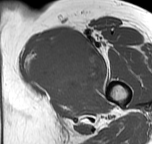
MRI of an extremity soft-tissue mass, one axial slice; position 41 of 57 along the scan axis; MR volume resampled by the dataset authors to the PET/CT grid (not the native acquisition matrix); 152 × 144 image matrix, field of view 148 × 141 mm. Female patient. From the clinical record (not read from this slice): histological type: pleiomorphic leiomyosarcoma; grade: intermediate; site of the primary tumour: left thigh.
Structures marked on this image (expert contour drawn on MRI and transferred to this co-registered scan by the dataset authors):
- gross tumour volume including surrounding oedema: box from (x=25, y=30) to (x=99, y=93) px
- gross tumour volume (mass): (x=25, y=30)–(x=99, y=93)